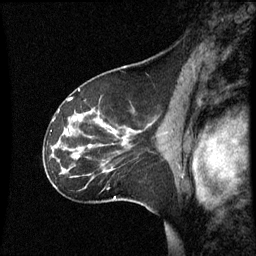
Breast MRI (dynamic contrast-enhanced), one sagittal slice. Position 39 of 60 along the scan axis. Dynamic contrast-enhanced series, image 2 of 3 at this slice position (ordered by acquisition). 1.5 T. TE 4.2 ms, TR 8.9 ms. 2 mm slice thickness. 256 × 256 image matrix. Patient: female, 45 years. From the clinical record (not read from this slice): setting: breast cancer imaged before/during neoadjuvant chemotherapy; receptor status: HR-positive, HER2-negative.
Annotated regions visible in this slice (semi-automatically segmented with operator editing):
- analysis volume of interest (the breast-tissue region the enhancement analysis was run in; not a lesion): bounding box [x1, y1, x2, y2] px = [46, 94, 171, 205]
- tumour enhancement mask (voxels above the 70 % enhancement threshold inside the analysis volume of interest): [90, 132, 129, 147]